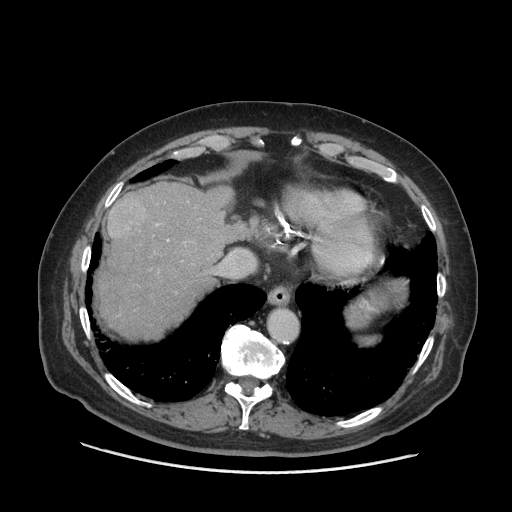
Contrast-enhanced abdominal CT (liver protocol), one axial slice. Position 59 of 77 along the scan axis. 140 kVp. Soft-tissue window (W 400 / L 40 HU). 2.5 mm slice thickness. 512 × 512 image matrix, field of view 420 × 420 mm. From the clinical record (not read from this slice): diagnosis: hepatocellular carcinoma (patient treated with transarterial chemoembolisation; whether this scan precedes or follows treatment is not stated here); TNM stage (as recorded): Stage-I; Child-Pugh class: A; tumour differentiation: well differentiated; tumour nodularity: uninodular.
Outlined on this slice (semi-automatically segmented with operator editing):
- abdominal aorta: box from (x=270, y=310) to (x=298, y=341) px
- liver parenchyma outside the tumour (the mass and vessels are separate outlines, so this box may not span the whole liver): (x=98, y=182)–(x=248, y=338)
- mass: (x=107, y=195)–(x=146, y=238)